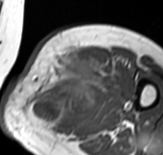
MRI of an extremity soft-tissue mass, one axial slice; position 43 of 65 along the scan axis; MR volume resampled by the dataset authors to the PET/CT grid (not the native acquisition matrix); 3.27 mm slice thickness; 163 × 155 image matrix, field of view 159 × 151 mm. Female patient. From the clinical record (not read from this slice): histological type: pleomorphic leiomyosarcoma; grade: high; site of the primary tumour: left thigh.
Outlined on this slice (expert contour drawn on MRI and transferred to this co-registered scan by the dataset authors):
- gross tumour volume including surrounding oedema: bounding box [x1, y1, x2, y2] px = [26, 51, 106, 134]
- gross tumour volume (mass): [46, 51, 95, 116]